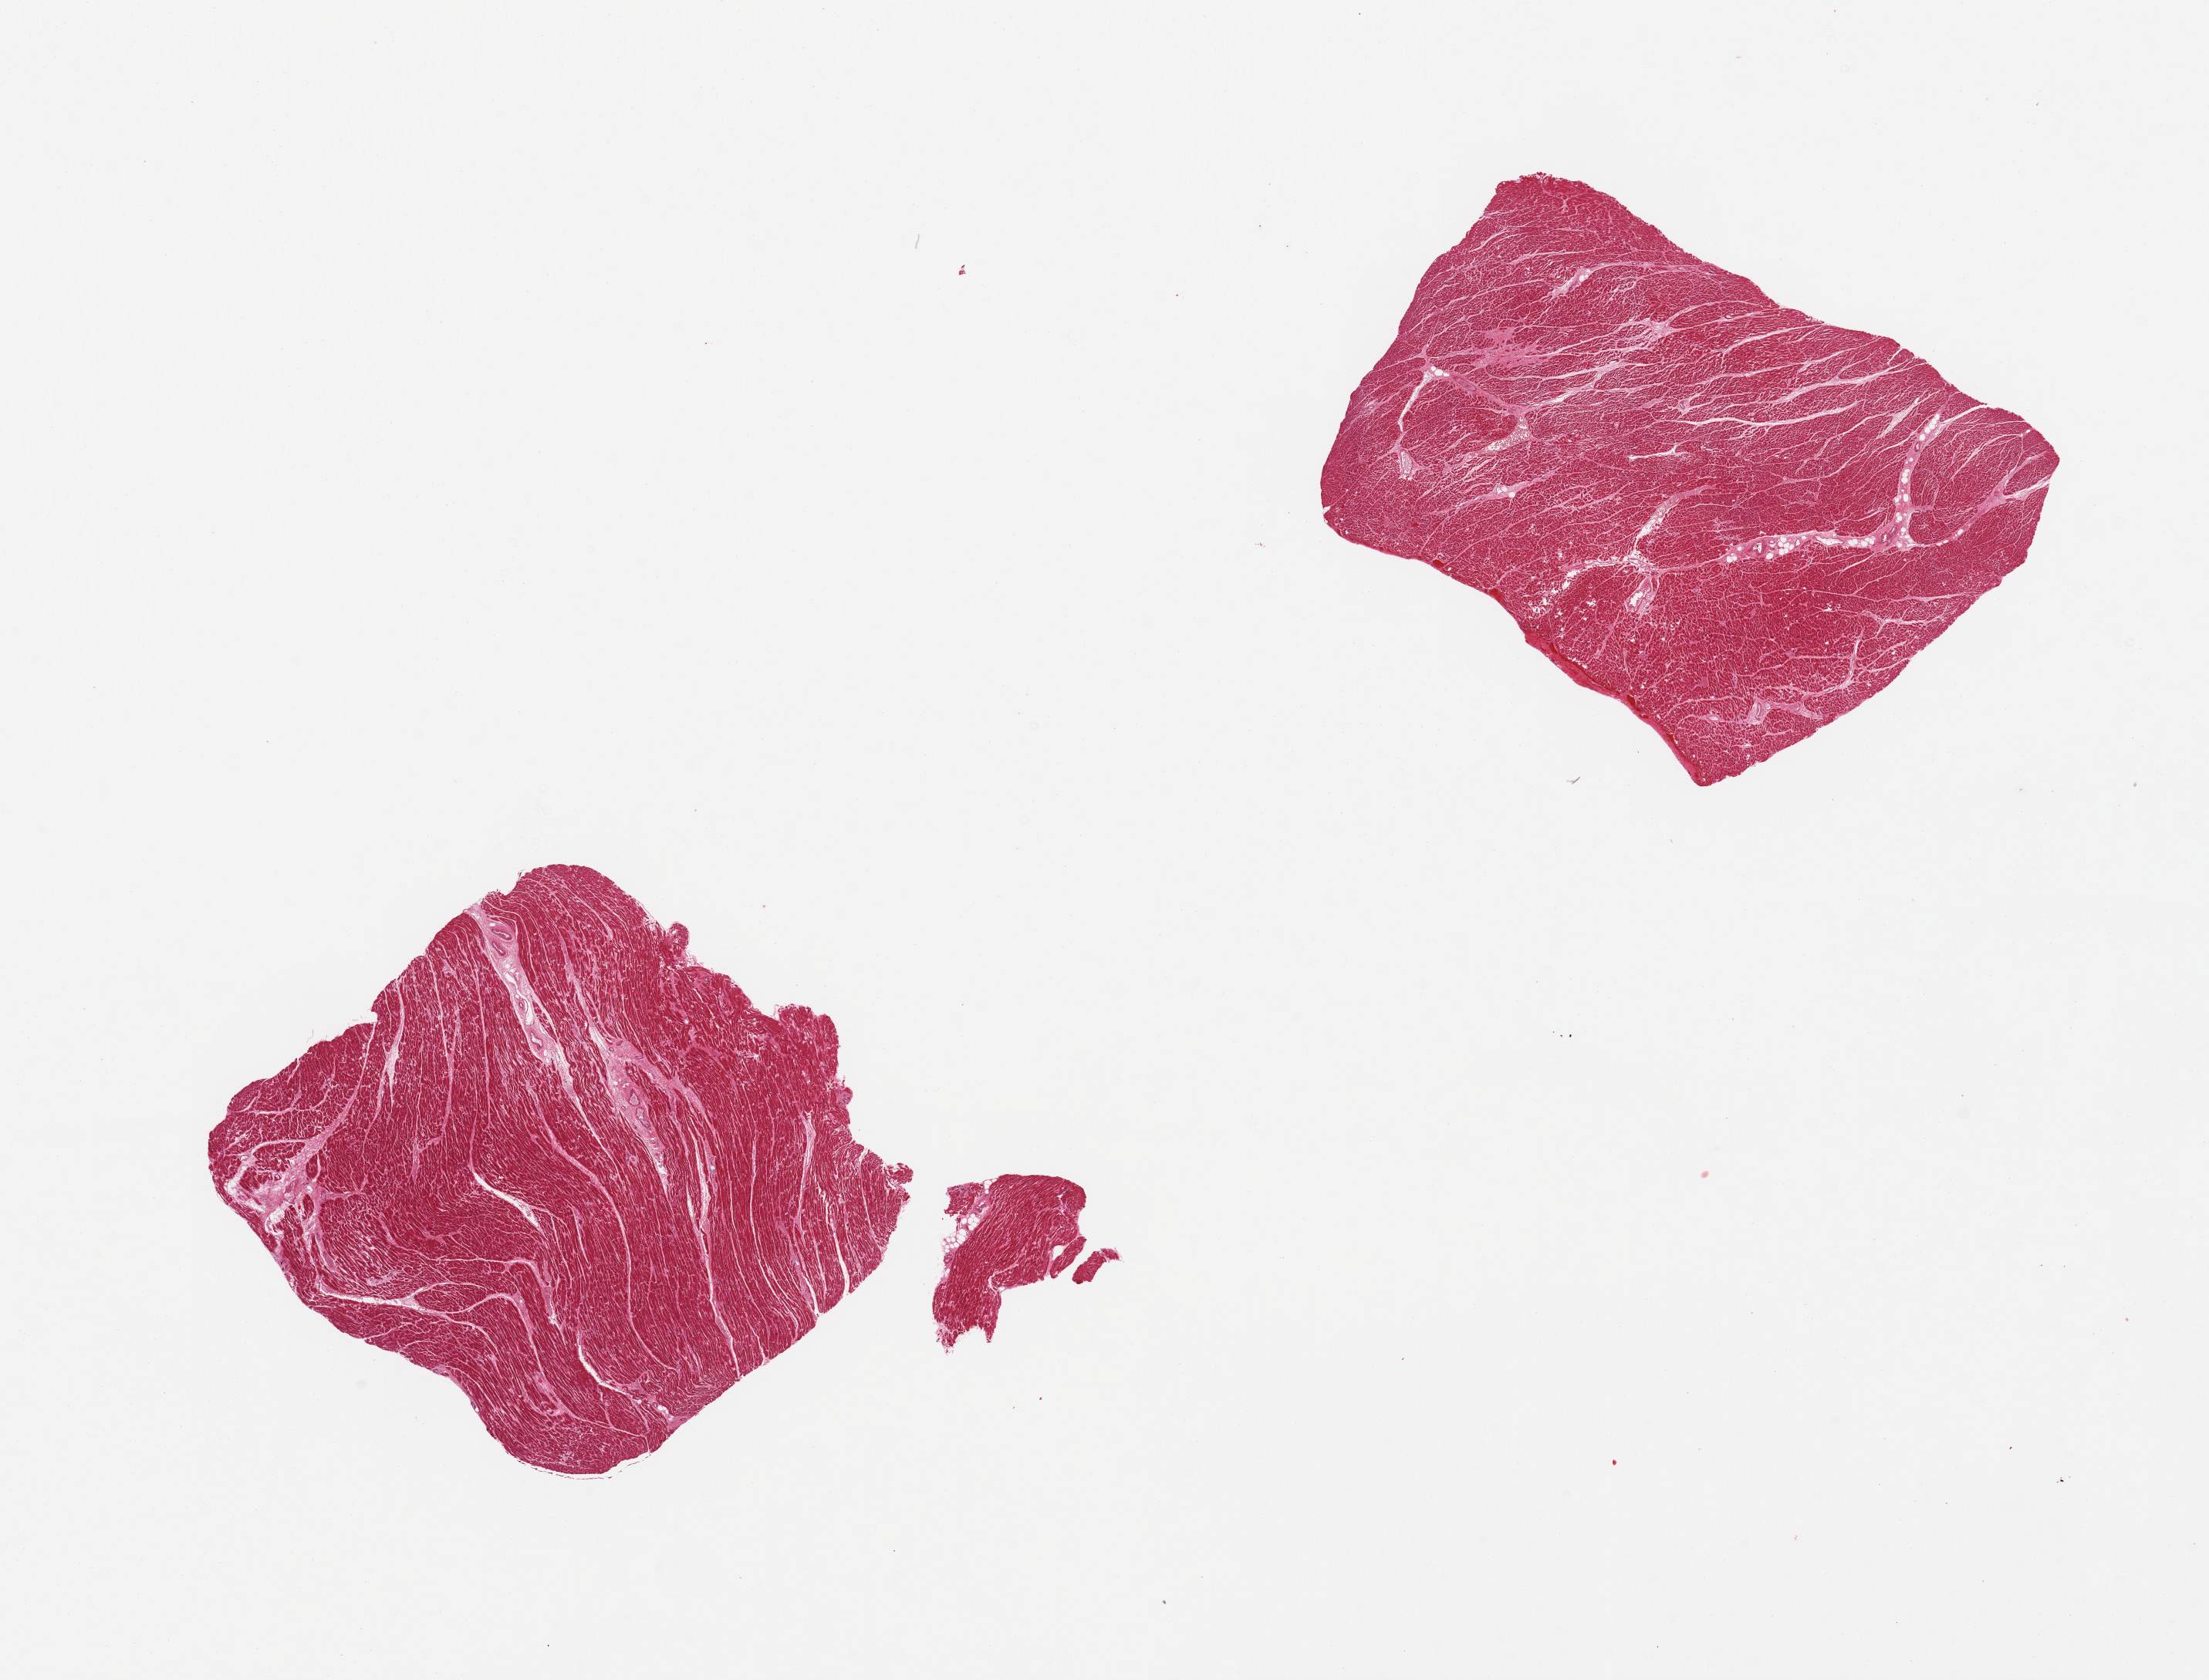
Whole-slide image, H&E stain — whole scanned area (about 22.6 x 17.2 mm, slide scanned at 20x) shown as a low-resolution overview, PAXgene-fixed, paraffin-embedded tissue, target tissue: heart, donor tissue sample. Donor sex: male.
Pathologist's review note for this sample: 2 pieces.